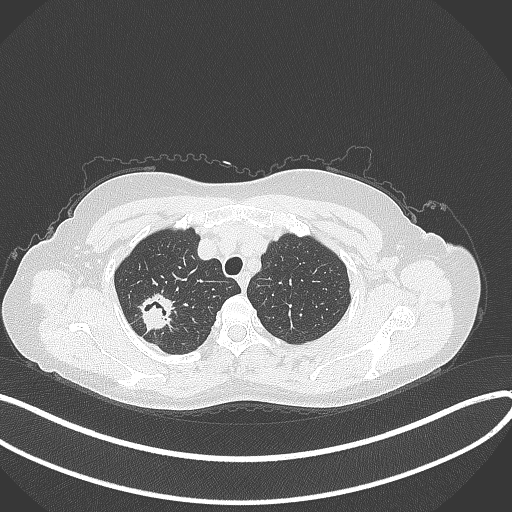
Chest CT, one axial slice; reconstruction kernel B70f; 120 kVp; lung window (W 1500 / L -600 HU); 512 × 512 image matrix, field of view 400 × 400 mm. Female patient, age 50 years. Case-level facts recorded for this patient, not image findings: clinical TNM (as recorded): T1c N0 M0; histopathological grade: G2-3.
Structures marked on this image (rectangle marked by the reading radiologist):
- lung tumour (recorded histology: adenocarcinoma): box from (x=133, y=288) to (x=180, y=336) px